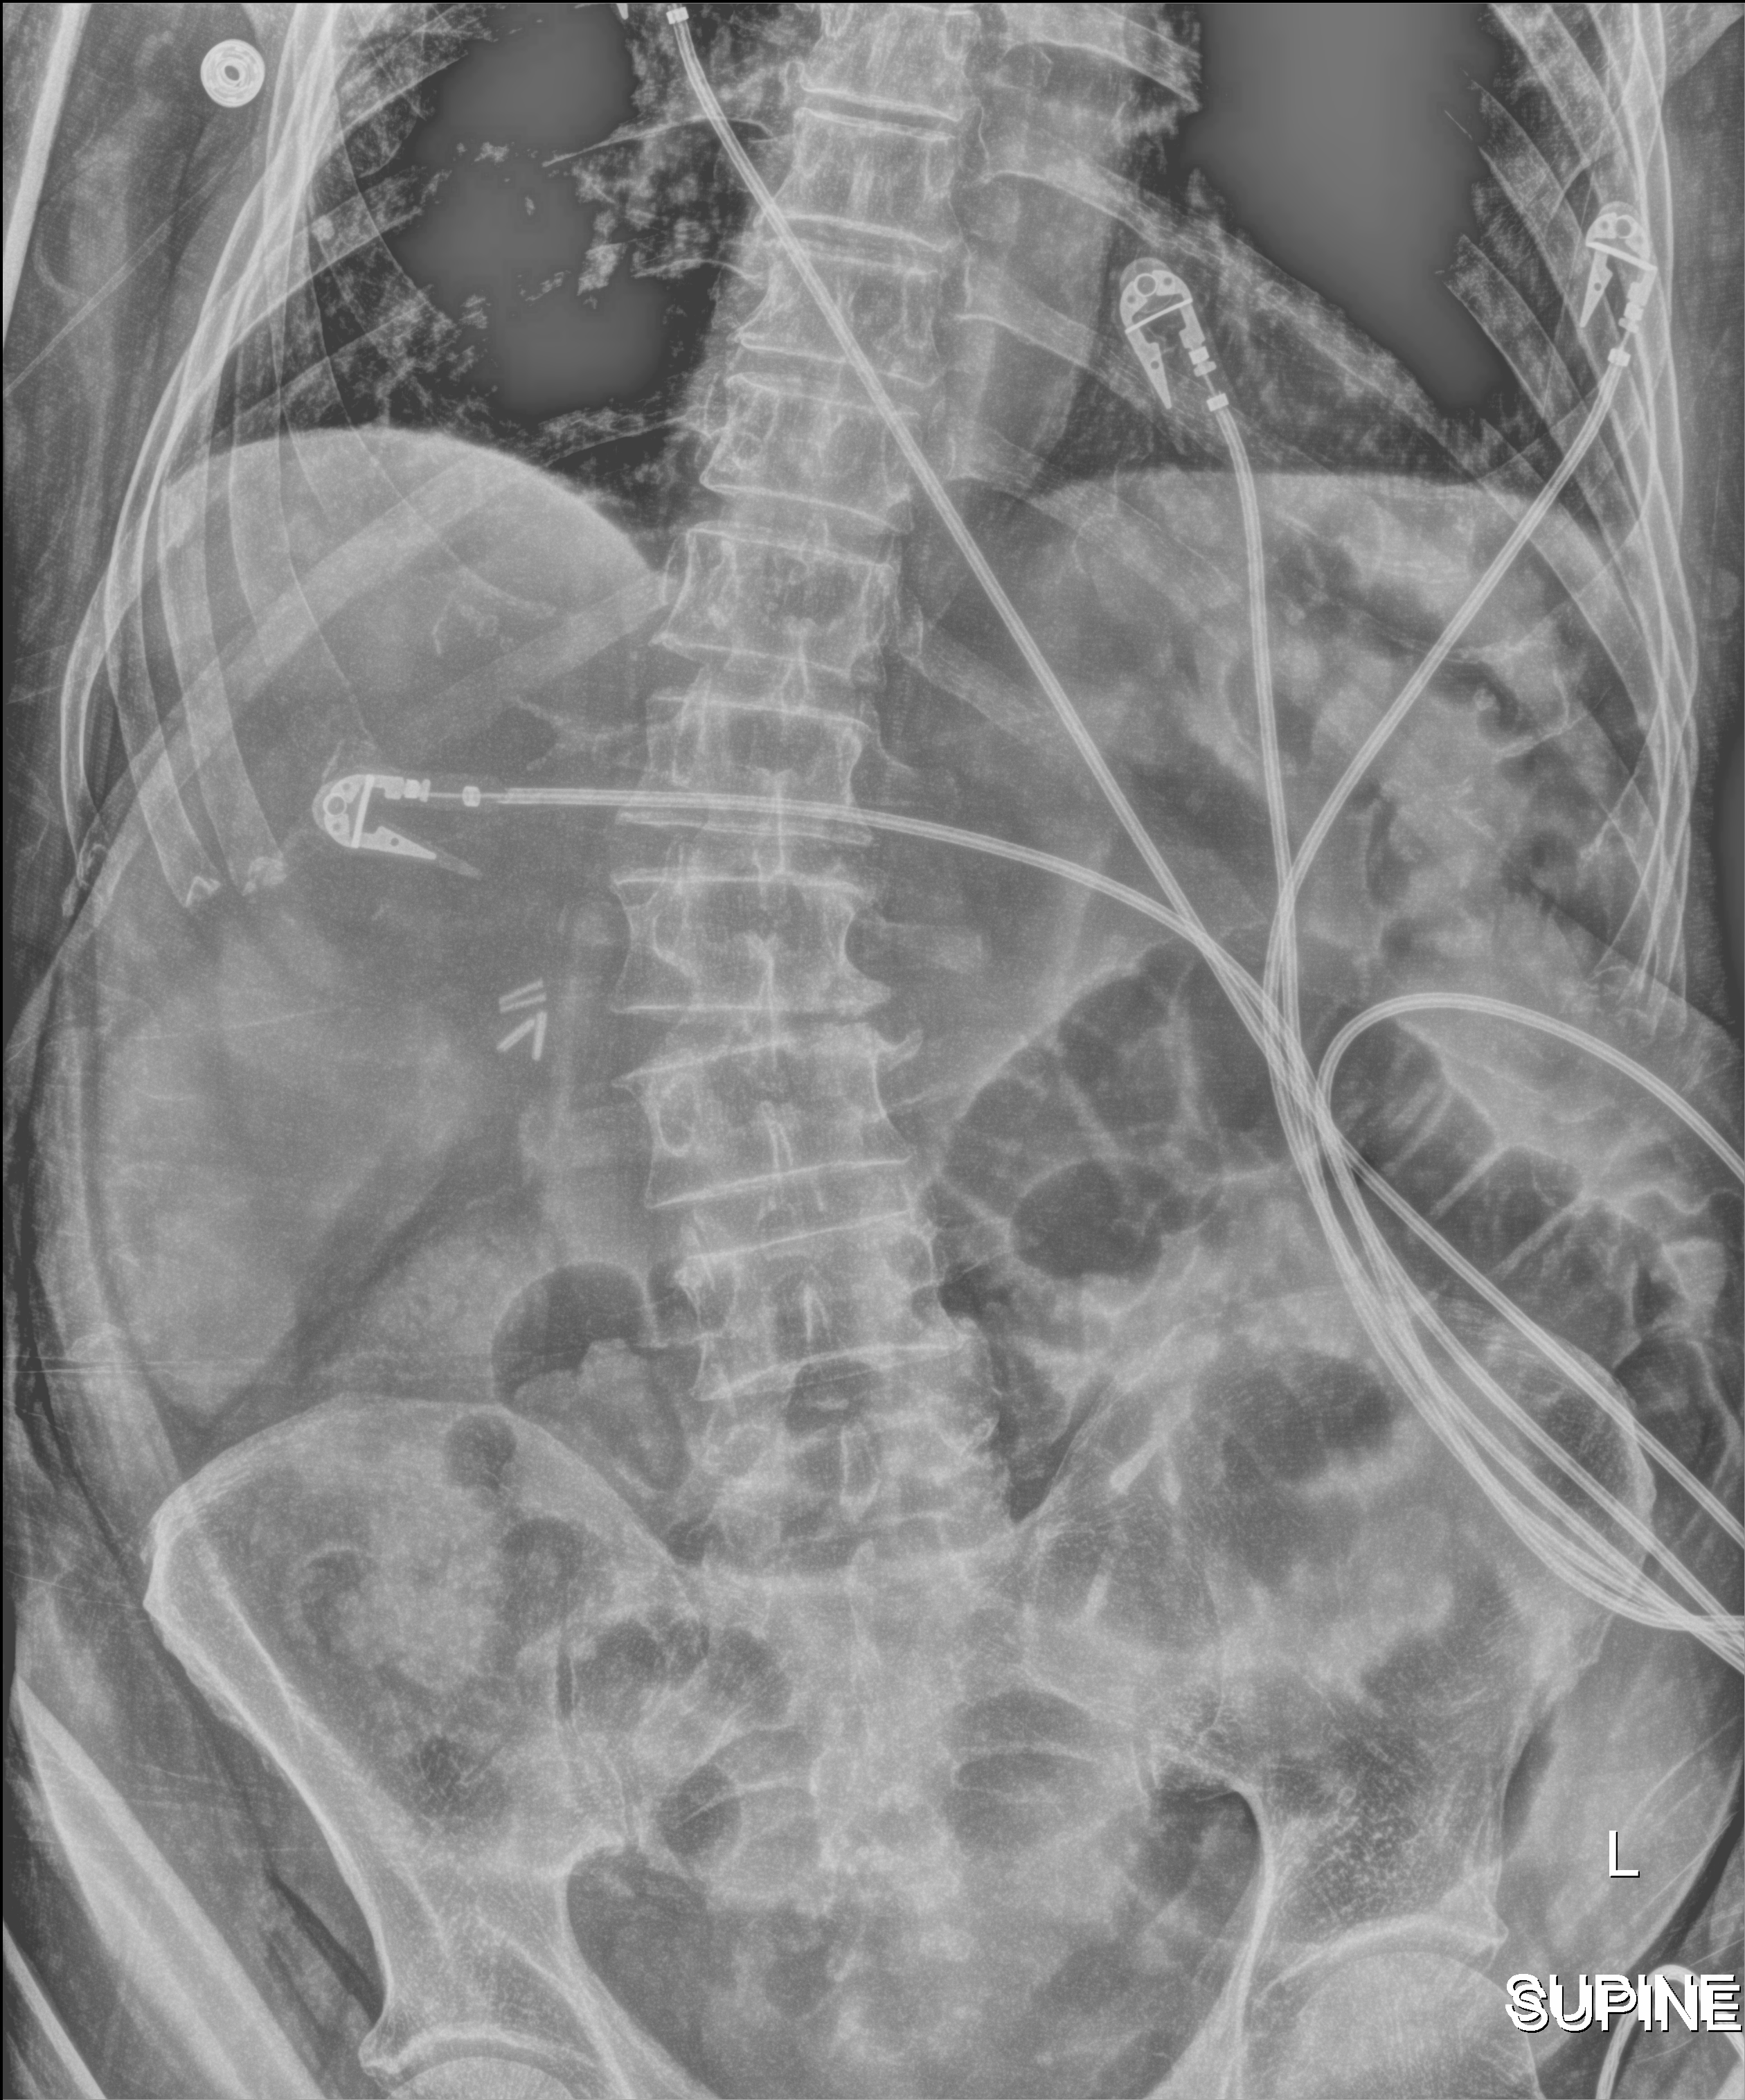
Abdomen X-ray (portable); anteroposterior (AP) projection. Patient hospitalised with COVID-19; male, aged 75–90 years.
From the hospital-stay record, not from the radiograph (when in the stay this image was taken is not recorded): admitted to intensive care during this hospital stay: yes; mechanically ventilated during this hospital stay: yes.